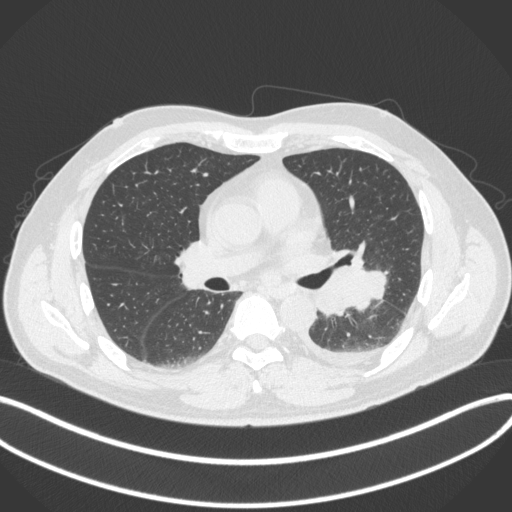
Chest CT, one axial slice. Slice 199 of 350 in the series (ordered by position). Lung window (W 1500 / L -600 HU). 1 mm slice thickness. 512 × 512 image matrix, field of view 400 × 400 mm. Male patient, age 58 years. Case-level facts recorded for this patient, not image findings: clinical TNM (as recorded): T3 N1 M1b; histopathological grade: G3.
Structures marked on this image (rectangle marked by the reading radiologist):
- lung tumour (recorded histology: small cell carcinoma): bounding box [x1, y1, x2, y2] px = [310, 262, 390, 321]